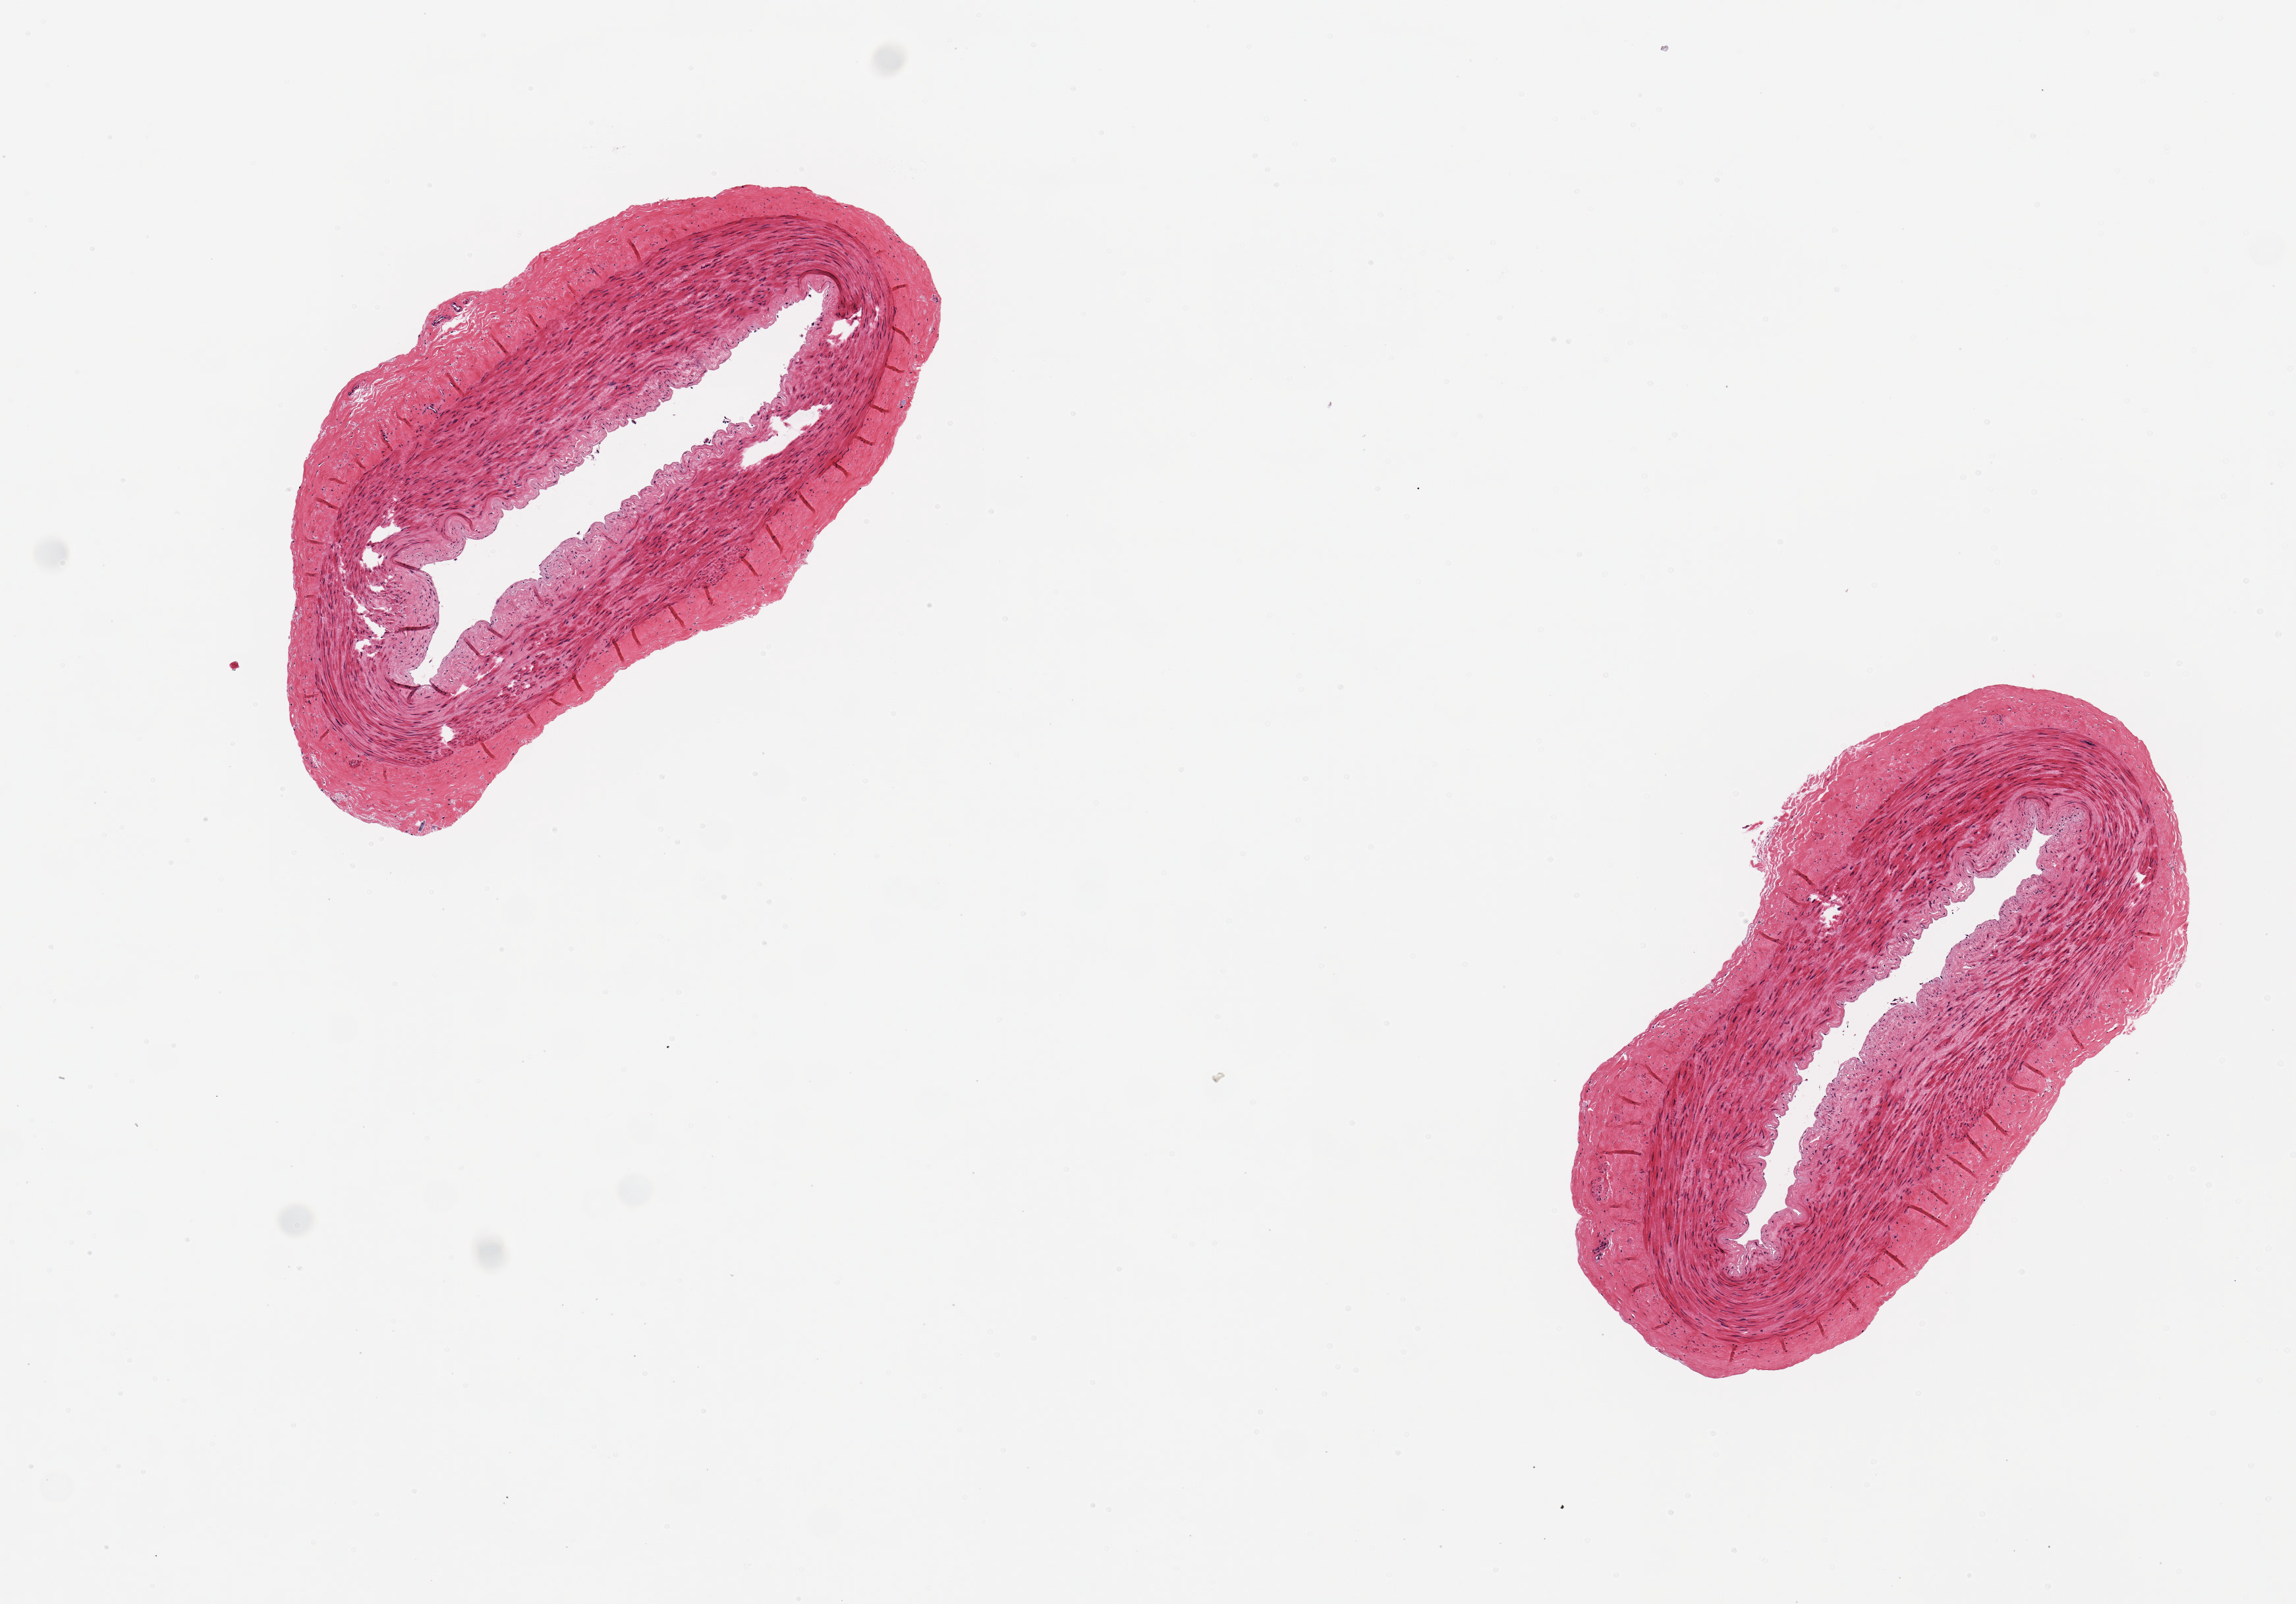
Digitized haematoxylin and eosin-stained section — low-resolution overview of the scanned area, about 6.9 x 4.8 mm, PAXgene-fixed paraffin-embedded (PFPE) section, sampled site (target tissue): tibial artery, donor tissue sample. Male donor.
Review note (as recorded): 2 ~2.3x1.2mm aliquots, good clean specimens.